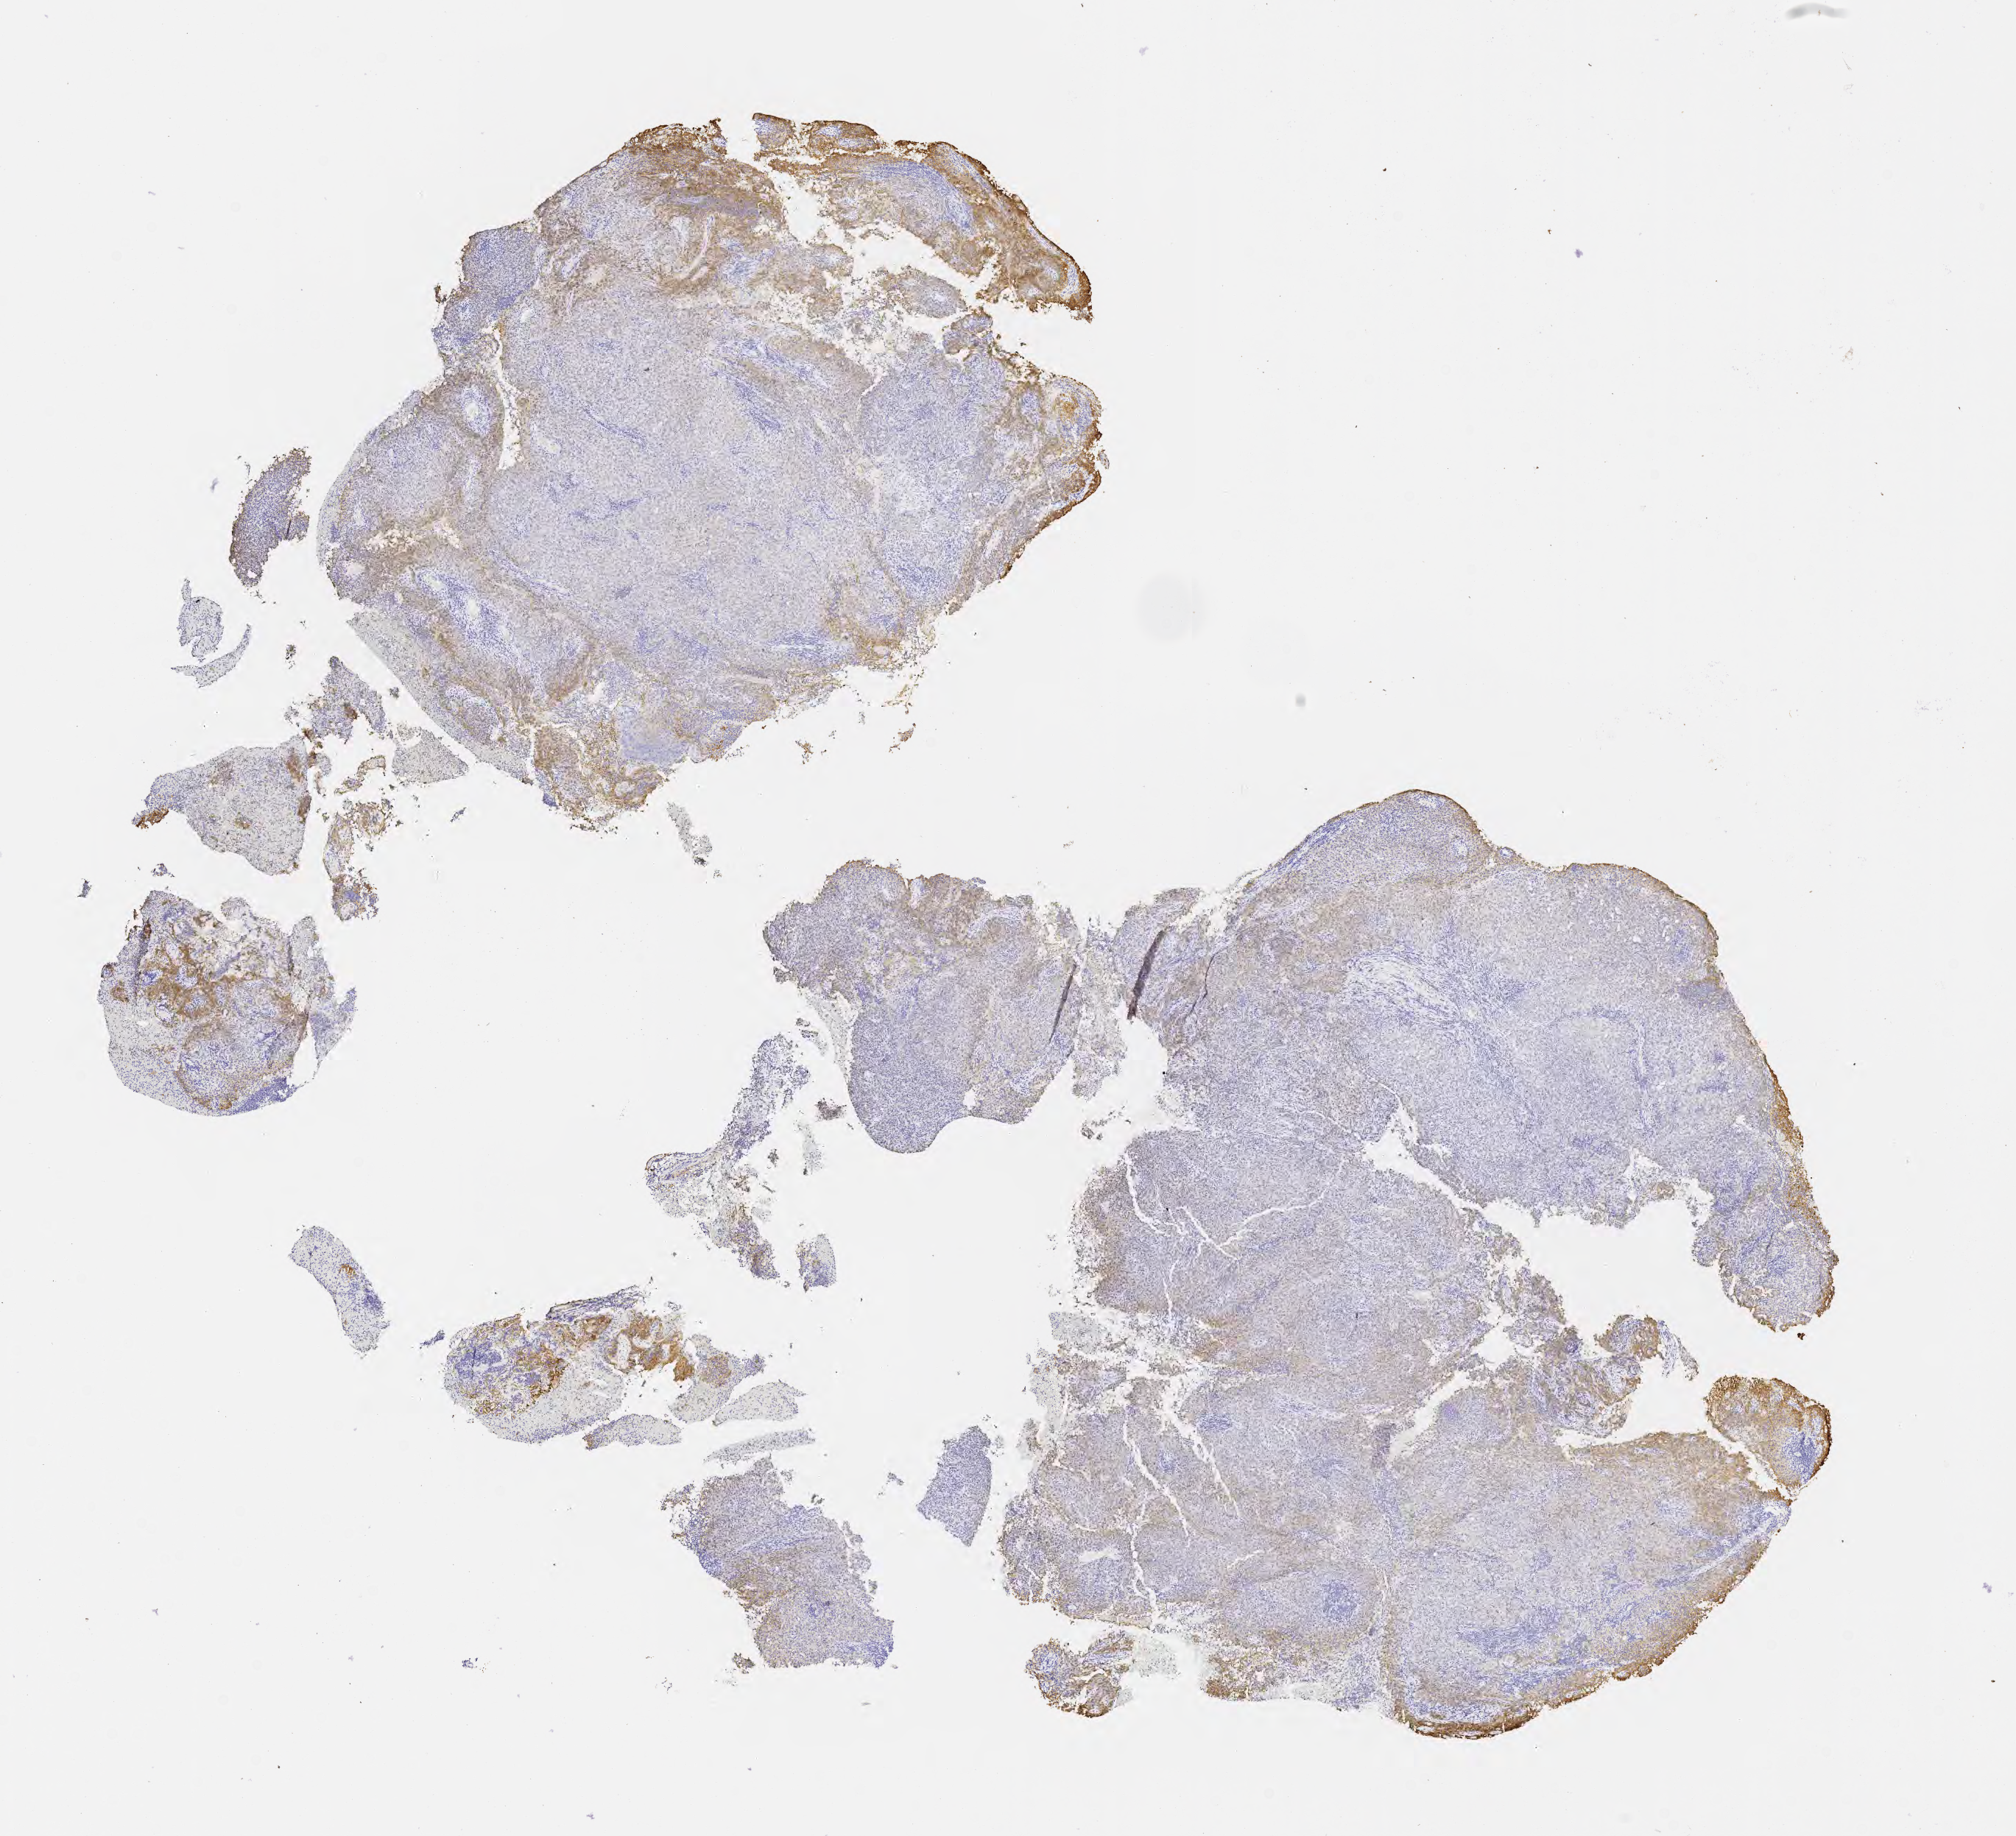
Immunohistochemistry (IHC) whole-slide image stained for MOC-31 (anti-EpCAM) — shown as a low-resolution overview of the whole scanned area (about 11.1 x 10.1 mm). Tumor tissue. Anatomic site: cervix. Patient: female, aged 70.
Diagnosis: Squamous cell carcinoma, large cell, nonkeratinizing, NOS.